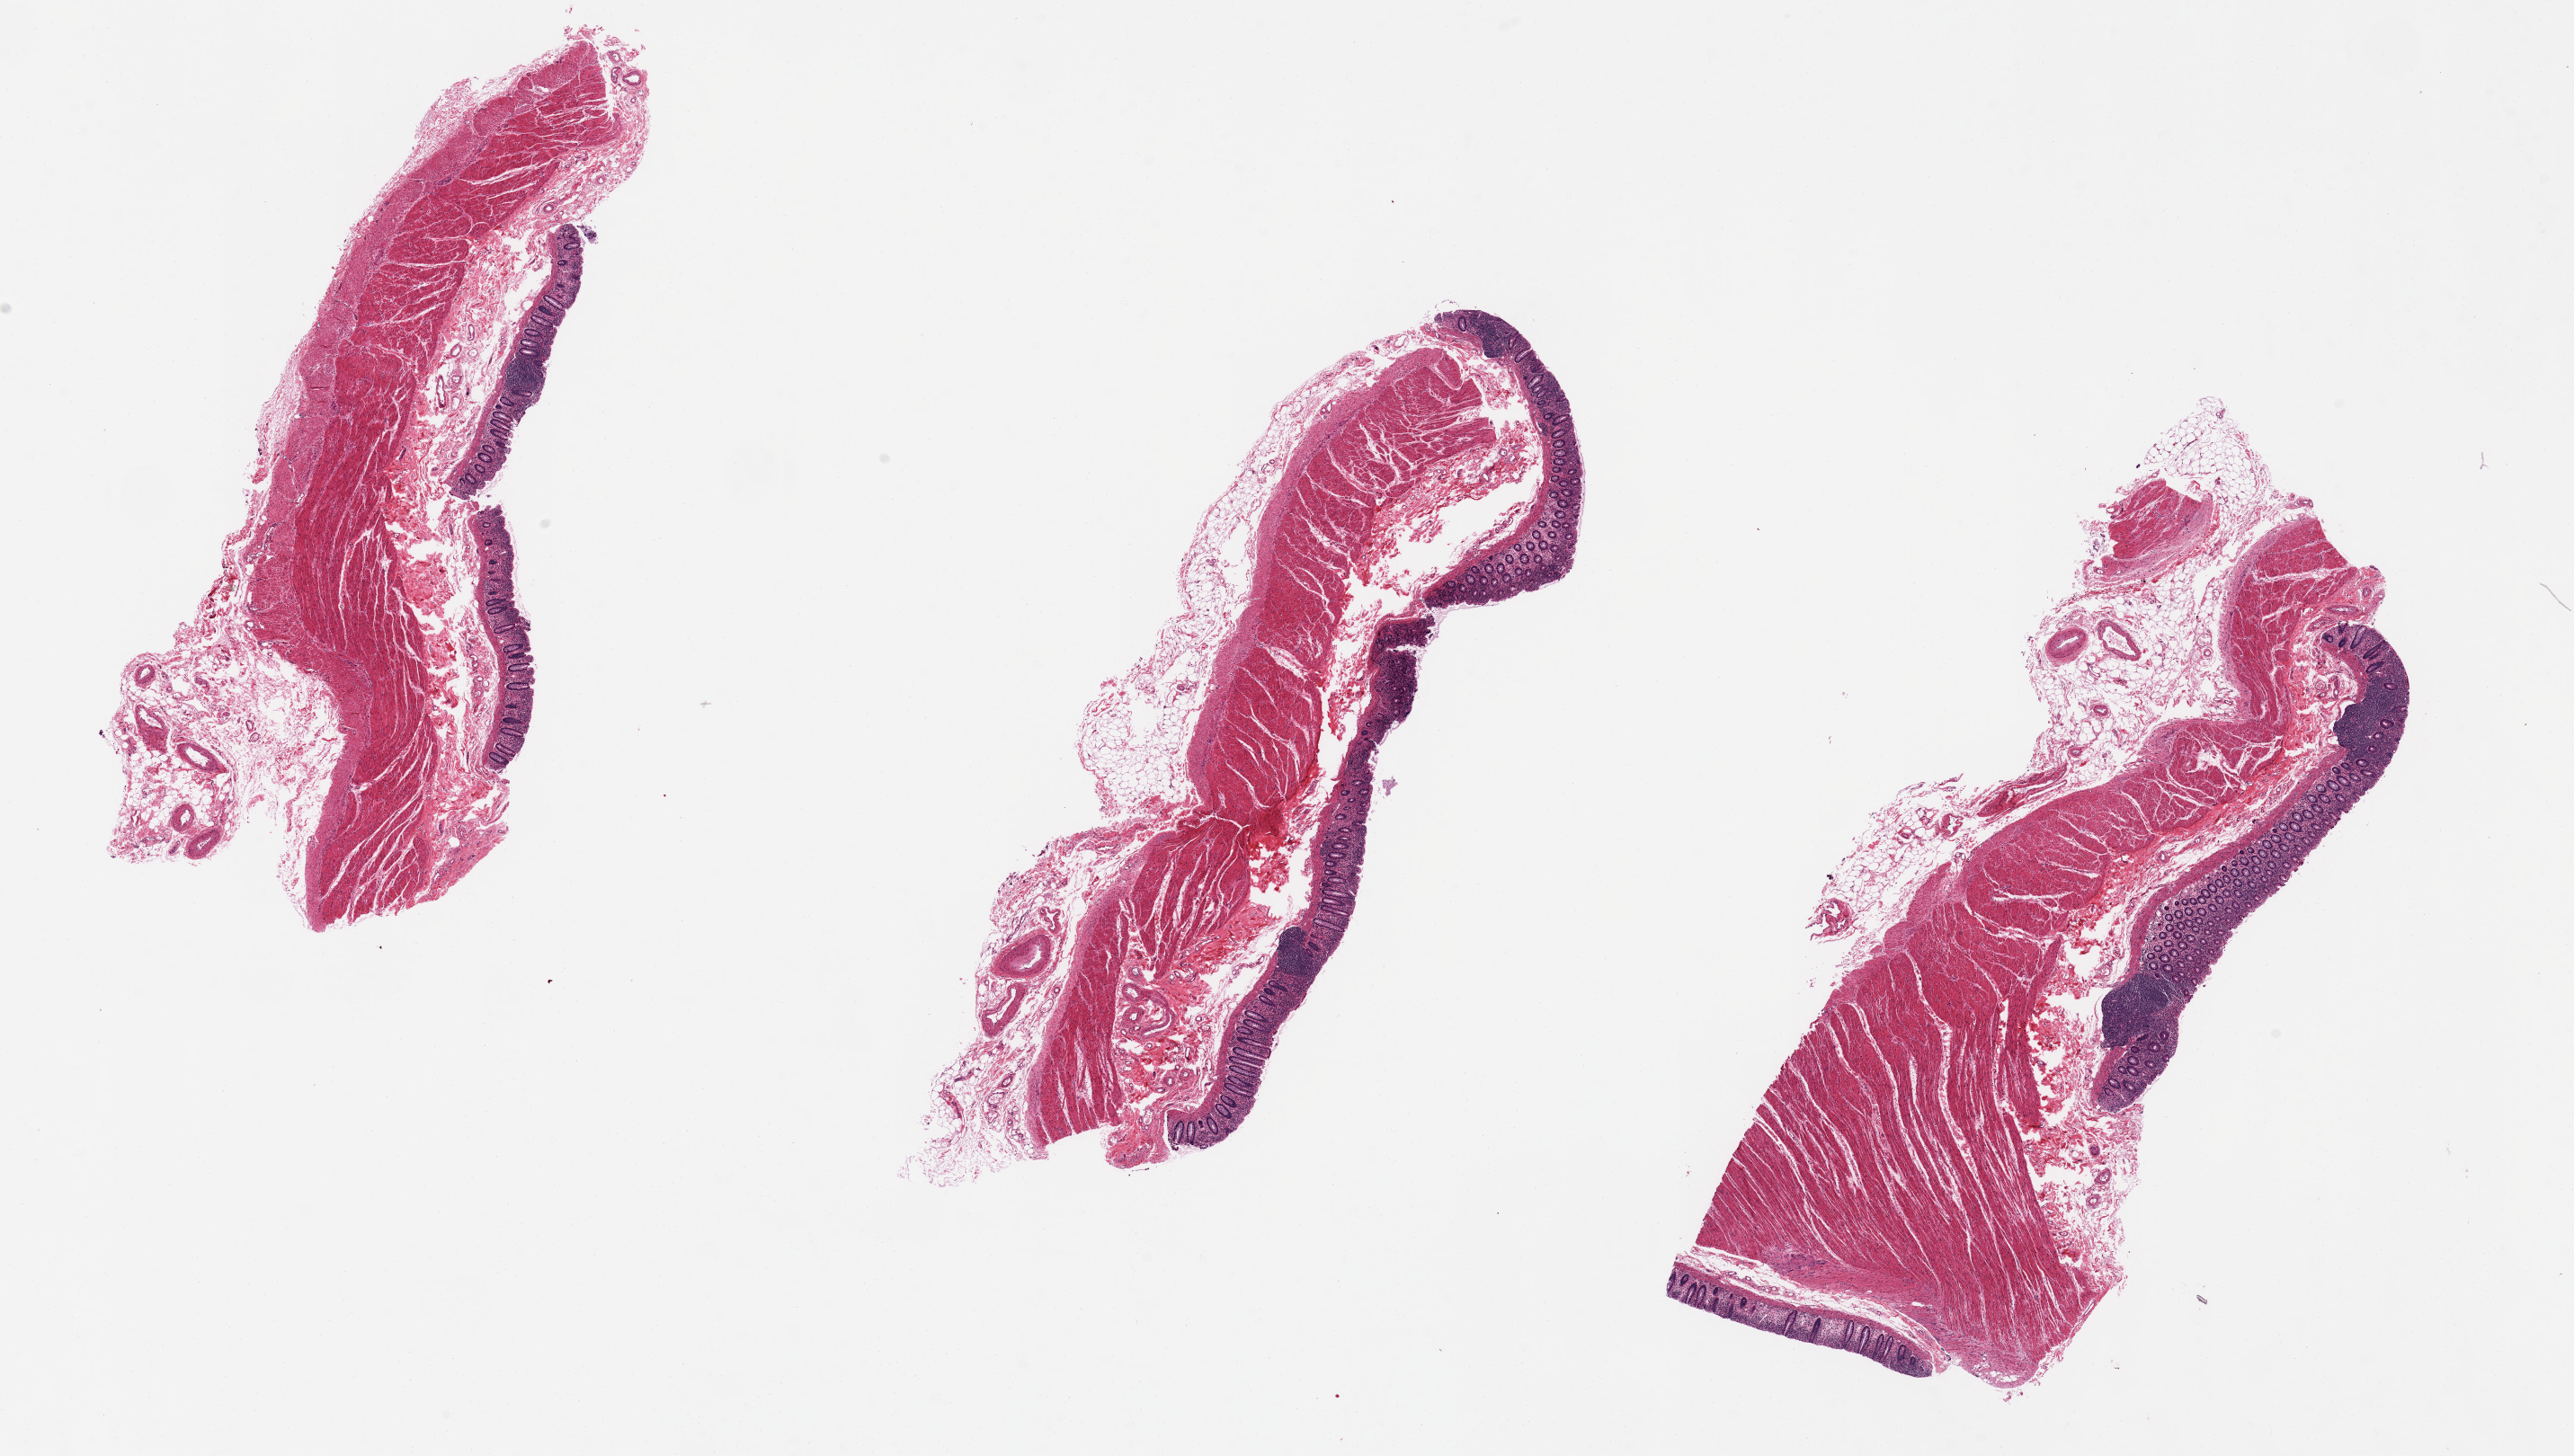
Haematoxylin and eosin whole-slide image — shown as a low-resolution overview of the whole scanned area (about 22.6 x 12.8 mm, from a 20x scan), PAXgene-fixed paraffin-embedded (PFPE) section, section of transverse colon (target tissue), donor tissue sample. Donor sex: female.
• reviewer comment on this tissue sample: some areas better preserved than others